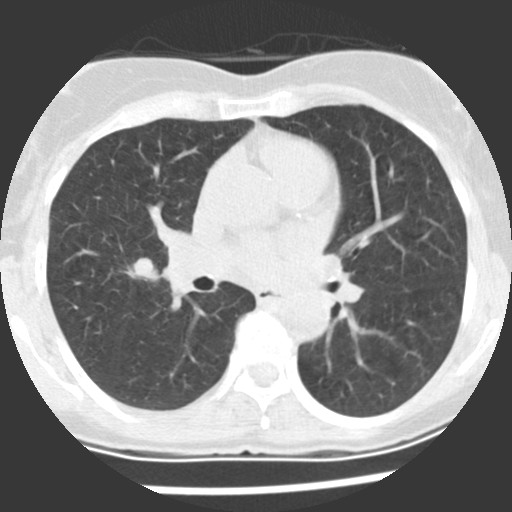
Low-dose screening chest CT, one axial slice; slice 120 of 225 in the series (ordered by position); reconstruction kernel STANDARD; lung window (W 1500 / L -600 HU); 2.5 mm slice thickness; 512 × 512 image matrix.
Outlined on this slice (outlined manually by an expert reader):
- lesion 1 (tumor, upper lobe of right lung): bounding box [x1, y1, x2, y2] px = [124, 258, 159, 282]